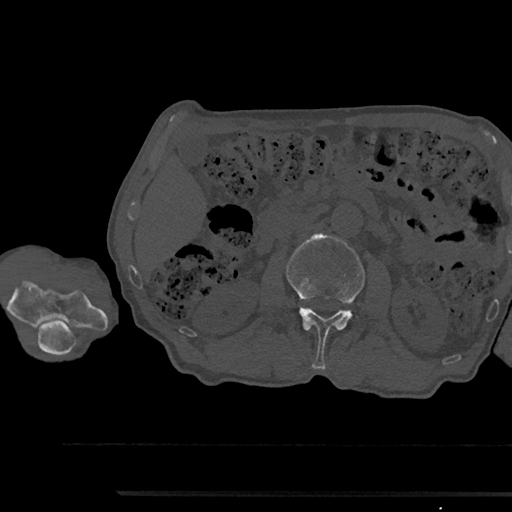
CT including the spine, one axial slice. Position 559 of 797 along the scan axis. 120 kVp. Bone window (W 1800 / L 400 HU). 0.5 mm slice thickness. 512 × 512 image matrix, field of view 367 × 367 mm. Male patient, age 79 years. Case-level facts recorded for this patient, not image findings: primary cancer: prostate.
Outlined on this slice (semi-automatically segmented with operator editing):
- L2 vertebra: box from (x=286, y=234) to (x=365, y=369) px